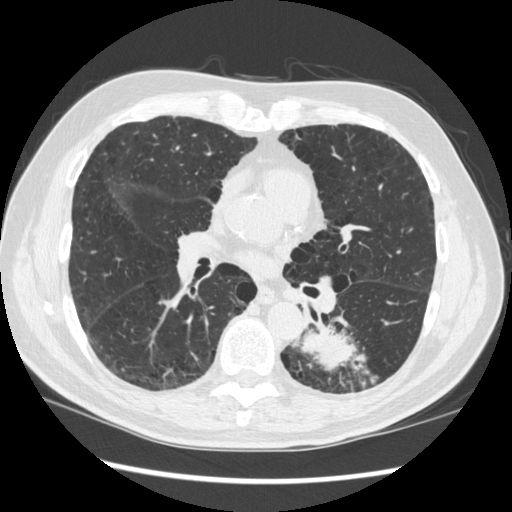
Low-dose screening chest CT, one axial slice; slice 165 of 348 in the series (ordered by position); lung window (W 1500 / L -600 HU); 512 × 512 image matrix, field of view 360 × 360 mm.
Structures marked on this image (outlined manually by an expert reader):
- lesion 1 (tumor, lower lobe of left lung): bounding box (x1, y1, x2, y2) in pixels: (298, 326, 373, 385)